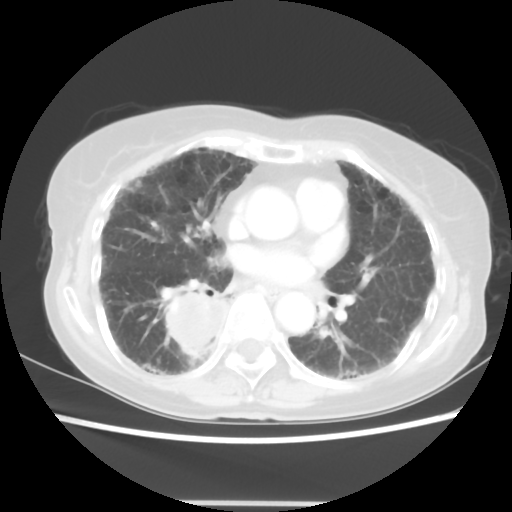
Chest CT, one axial slice. Position 26 of 52 along the scan axis. Lung window (W 1500 / L -600 HU). 512 × 512 image matrix, field of view 325 × 325 mm. Patient: female, 71 years. From the clinical record (not read from this slice): clinical TNM (as recorded): T3 N0 M0.
Outlined on this slice (rectangle marked by the reading radiologist):
- lung tumour (recorded histology: squamous cell carcinoma): bounding box [x1, y1, x2, y2] px = [157, 286, 231, 365]